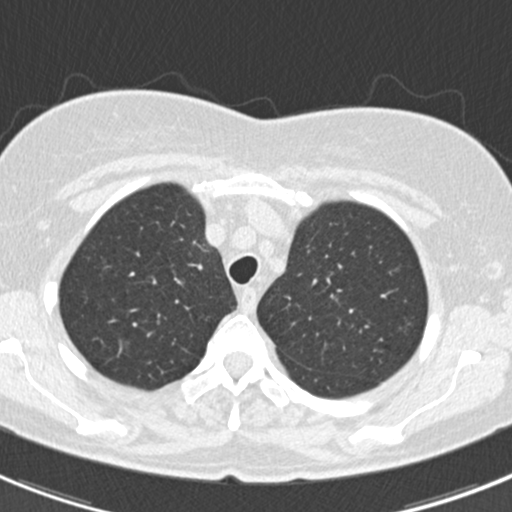
Axial slice from a low-dose chest CT screening exam. First (baseline) screen. Lung window (W 1500 / L -600 HU). Slice 42 of 184 in the series. 512 × 512 image matrix. Female participant, aged 60 years at enrolment. Current smoker at enrolment.
Expert reader's lesion annotation, bounding box <380,309,421,343> (left, top, right, bottom; pixels). The screening reader recorded 3 non-calcified nodules or masses ≥4 mm on this exam; which of them this box marks is not recorded. Official screen result: positive, change unspecified: nodule(s) >= 4 mm or enlarging nodule(s), mass(es), or other non-specific abnormalities suspicious for lung cancer. Later outcome: lung cancer diagnosed 886 days after this screen — non-small cell carcinoma, left upper lobe, poorly differentiated (G3), stage IB (AJCC 6th edition), 7 mm at pathology.